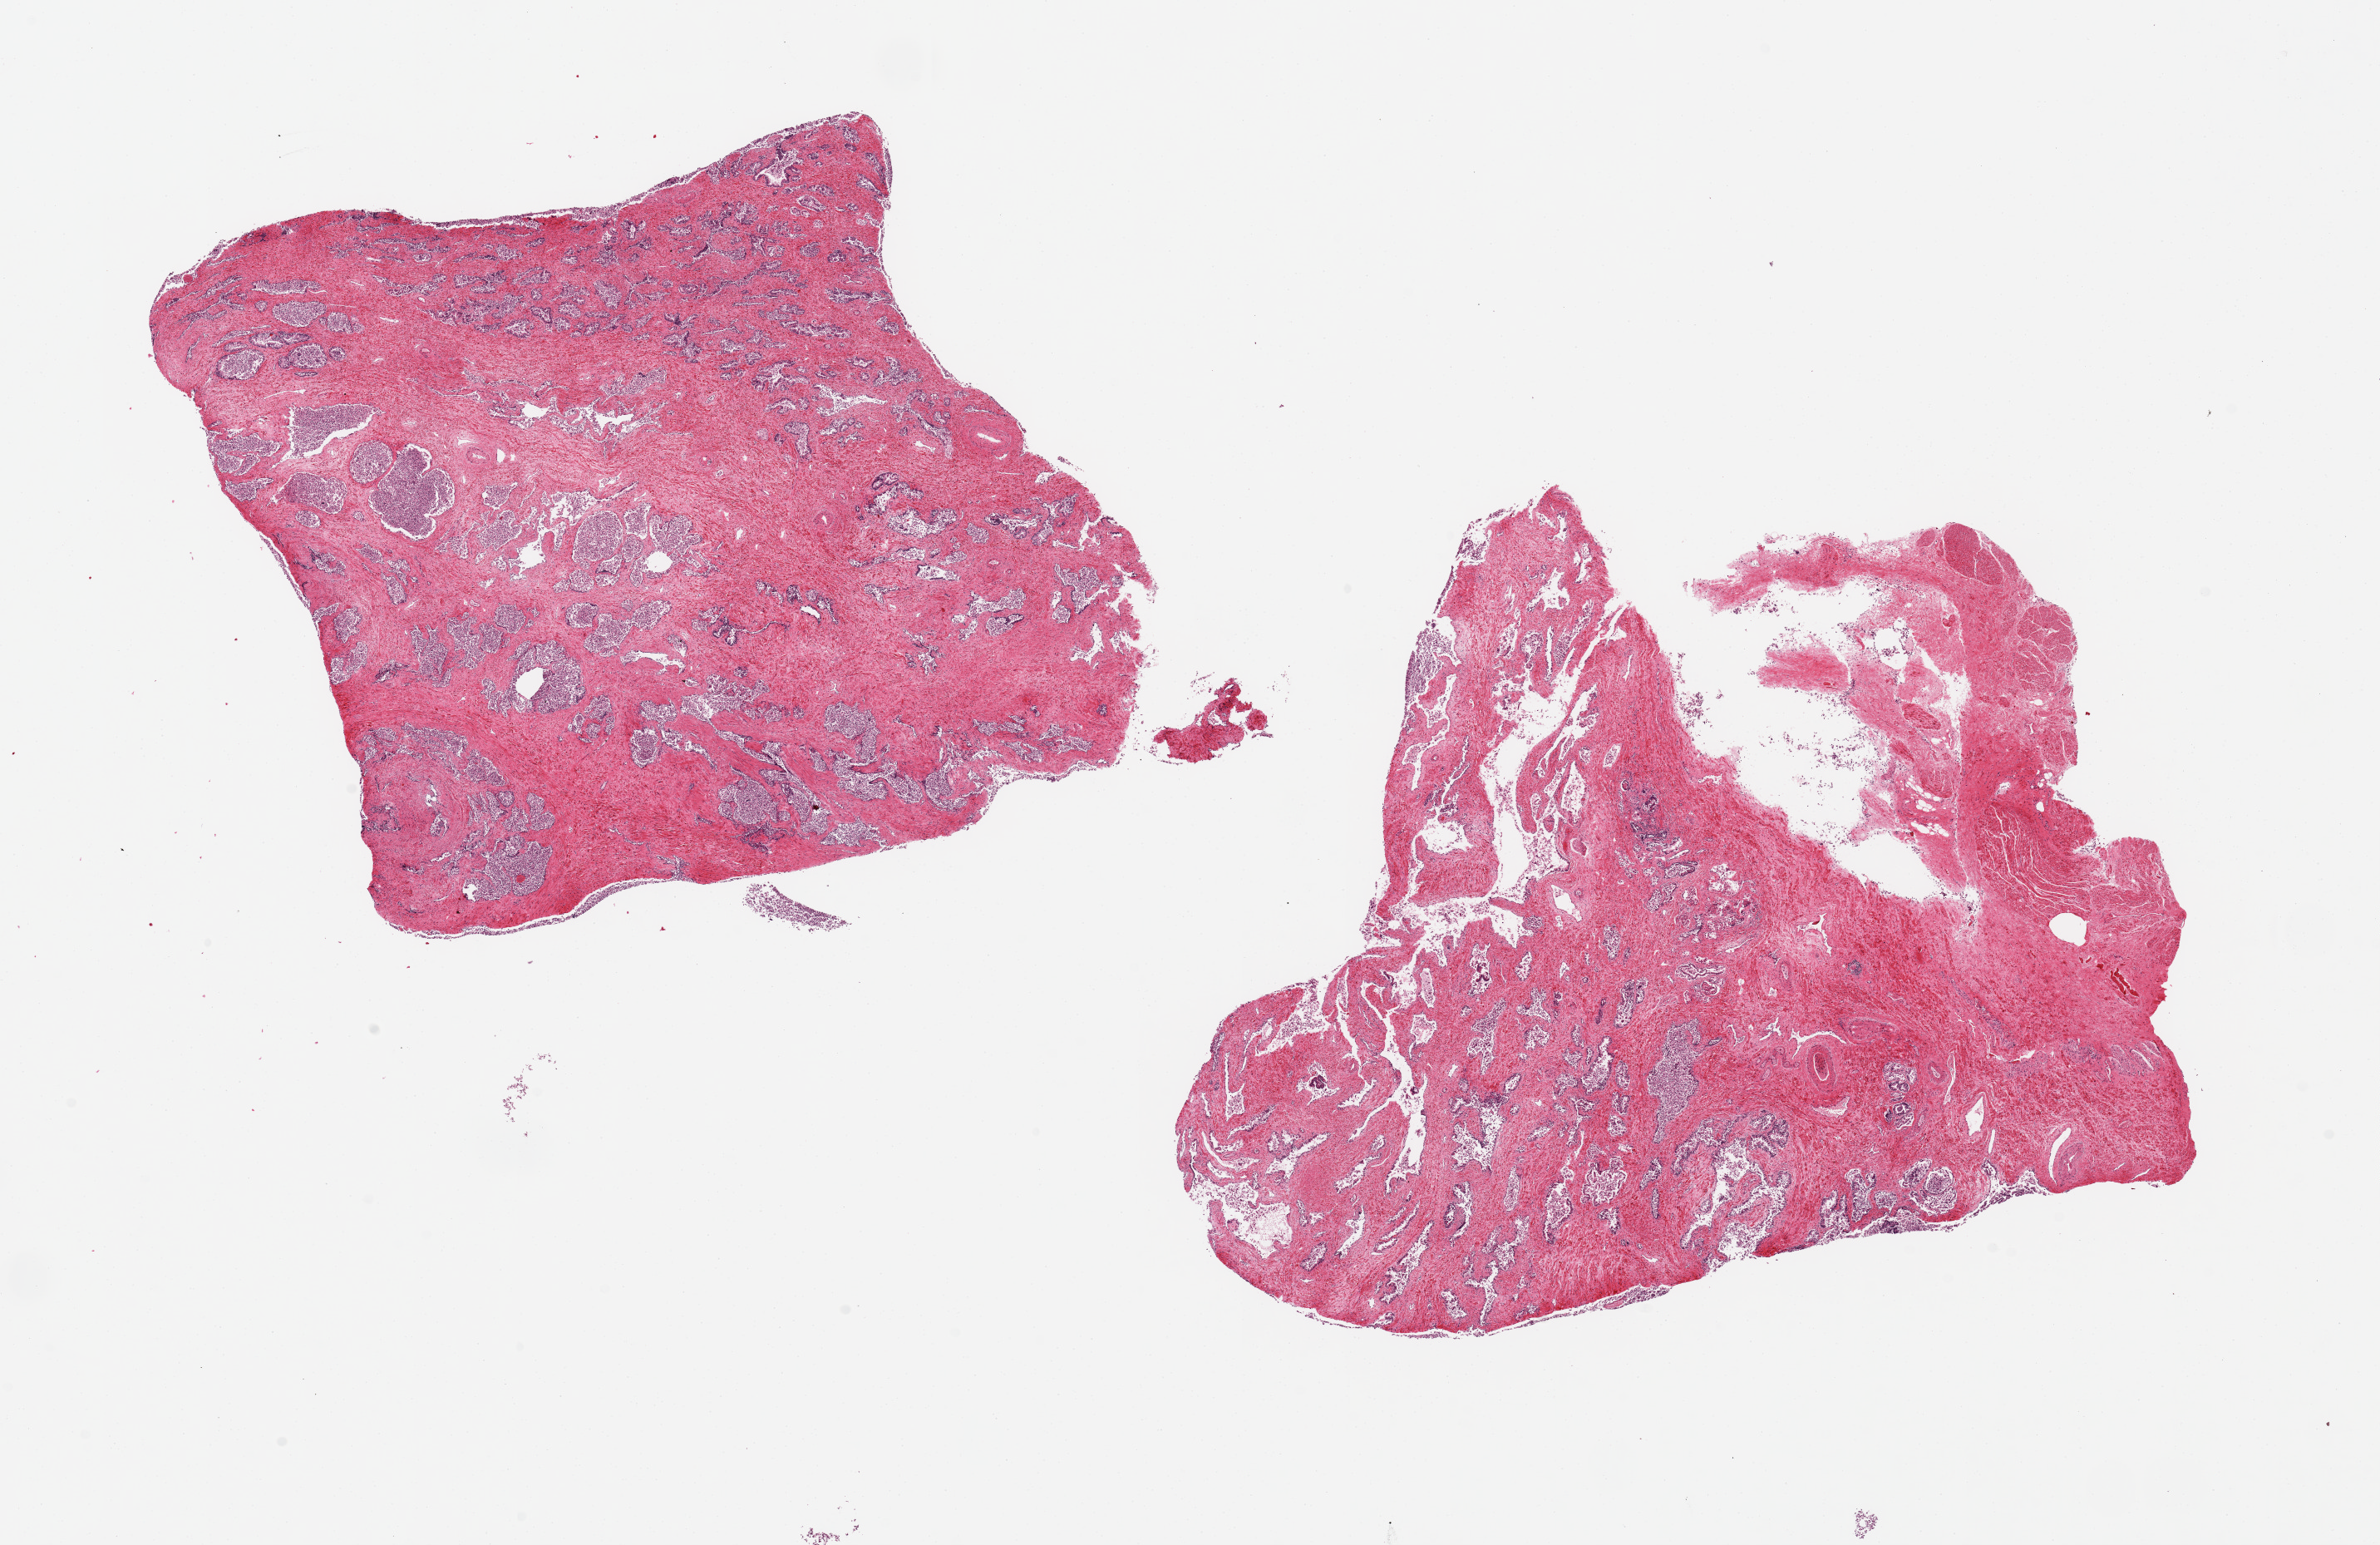
Digitized haematoxylin and eosin-stained section — shown as a low-resolution overview of the whole scanned area (about 22.6 x 14.7 mm, slide scanned at 20x), PAXgene-fixed, paraffin-embedded tissue, target tissue: prostate, tissue donor sample. Donor: male.
• pathologist's review note for this sample: 2 pieces ~8x7mm, glandular mucosa badly autolyzed, probable glandular hyperplasia based on pattern